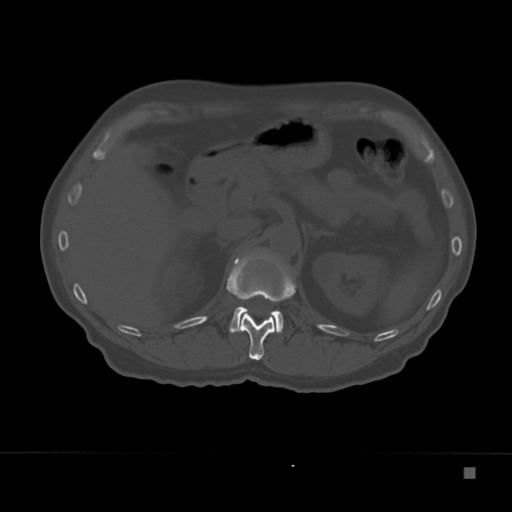
CT including the spine, one axial slice; position 123 of 332 along the scan axis; reconstruction kernel Br40s; bone window (W 1800 / L 400 HU); 1.5 mm slice thickness; 512 × 512 image matrix, field of view 389 × 389 mm. Male patient, age 72 years. Case-level facts recorded for this patient, not image findings: primary cancer: skeletal.
Outlined on this slice (semi-automatically segmented with operator editing):
- L1 vertebra: bounding box <229,307,283,333> (left, top, right, bottom; pixels)
- T12 vertebra: <226,253,296,360>